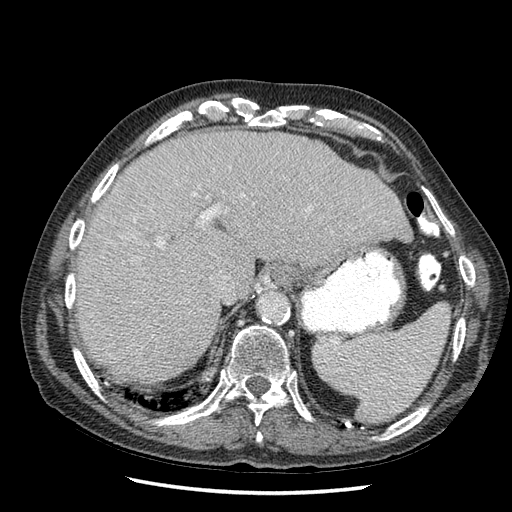
Contrast-enhanced abdominal CT (liver protocol), one axial slice; position 42 of 67 along the scan axis; 120 kVp; soft-tissue window (W 400 / L 40 HU); 512 × 512 image matrix. From the clinical record (not read from this slice): diagnosis: hepatocellular carcinoma (patient treated with transarterial chemoembolisation; whether this scan precedes or follows treatment is not stated here); TNM stage (as recorded): Stage-I; Child-Pugh class: A; tumour differentiation: moderately differentiated.
Annotated regions visible in this slice (semi-automatic segmentation, software-assisted and operator-edited):
- liver parenchyma outside the tumour (the mass and vessels are separate outlines, so this box may not span the whole liver): bounding box [x1, y1, x2, y2] px = [76, 128, 410, 384]
- liver vessels: [121, 185, 332, 339]